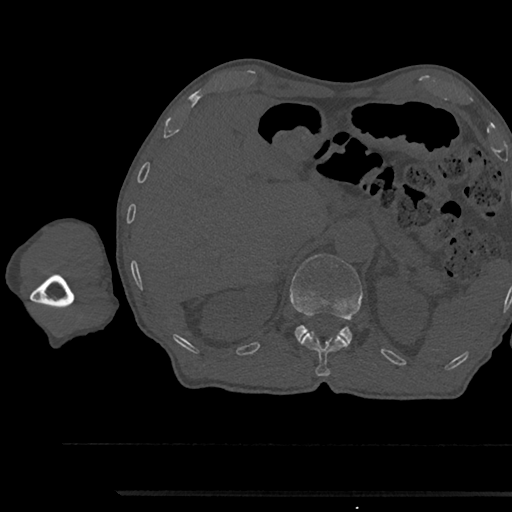
CT including the spine, one axial slice; position 678 of 797 along the scan axis; reconstruction kernel Br40s/3; 120 kVp; bone window (W 1800 / L 400 HU); 0.5 mm slice thickness; 512 × 512 image matrix, field of view 367 × 367 mm. Patient: male, 79 years. From the clinical record (not read from this slice): primary cancer: prostate.
Structures marked on this image (semi-automatically segmented with operator editing):
- L1 vertebra: bounding box (x1, y1, x2, y2) in pixels: (290, 254, 362, 342)
- T12 vertebra: (300, 331, 349, 376)